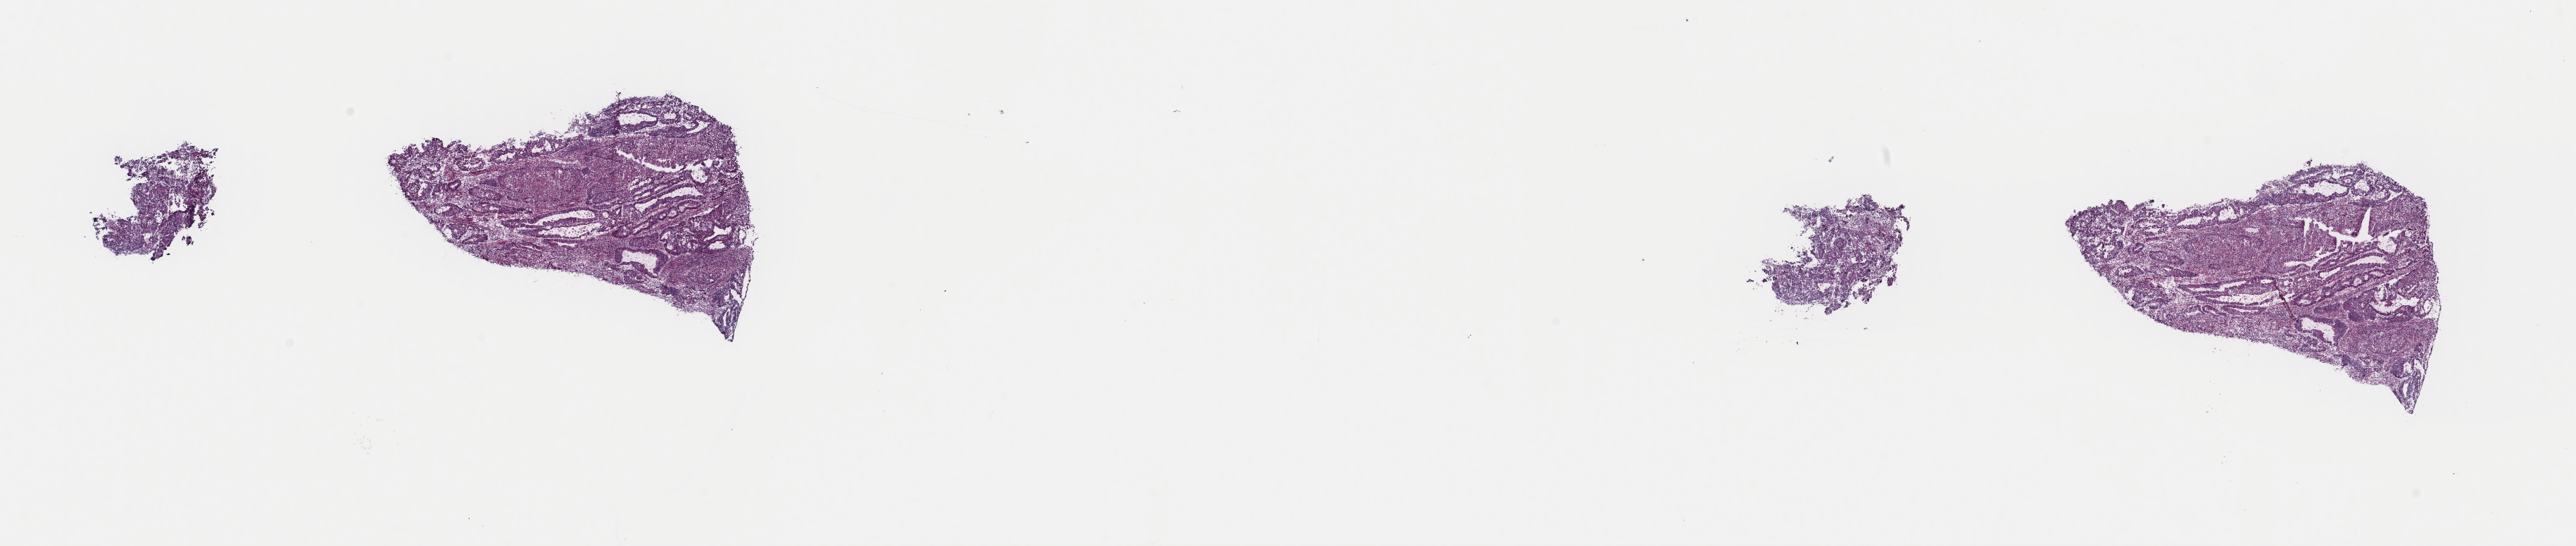
Digitized H&E tissue section (whole slide), whole scanned area (about 28.9 x 6.1 mm, acquisition: 40x scan) shown as a low-resolution overview; frozen section; sample: primary tumour, uterus. Patient: female, age at initial diagnosis 61 years. Histologic grade: G2 (moderately differentiated). Slide review estimates, as recorded: tumour cells 70%, tumour nuclei 70%, normal cells 0%, stromal cells 20%, necrosis 10%. Inflammatory infiltration, as recorded: lymphocyte infiltration 40%, monocyte infiltration 20%, neutrophil infiltration 20%.
* FIGO stage: IIIB
* histologic diagnosis: Endometrioid adenocarcinoma, NOS